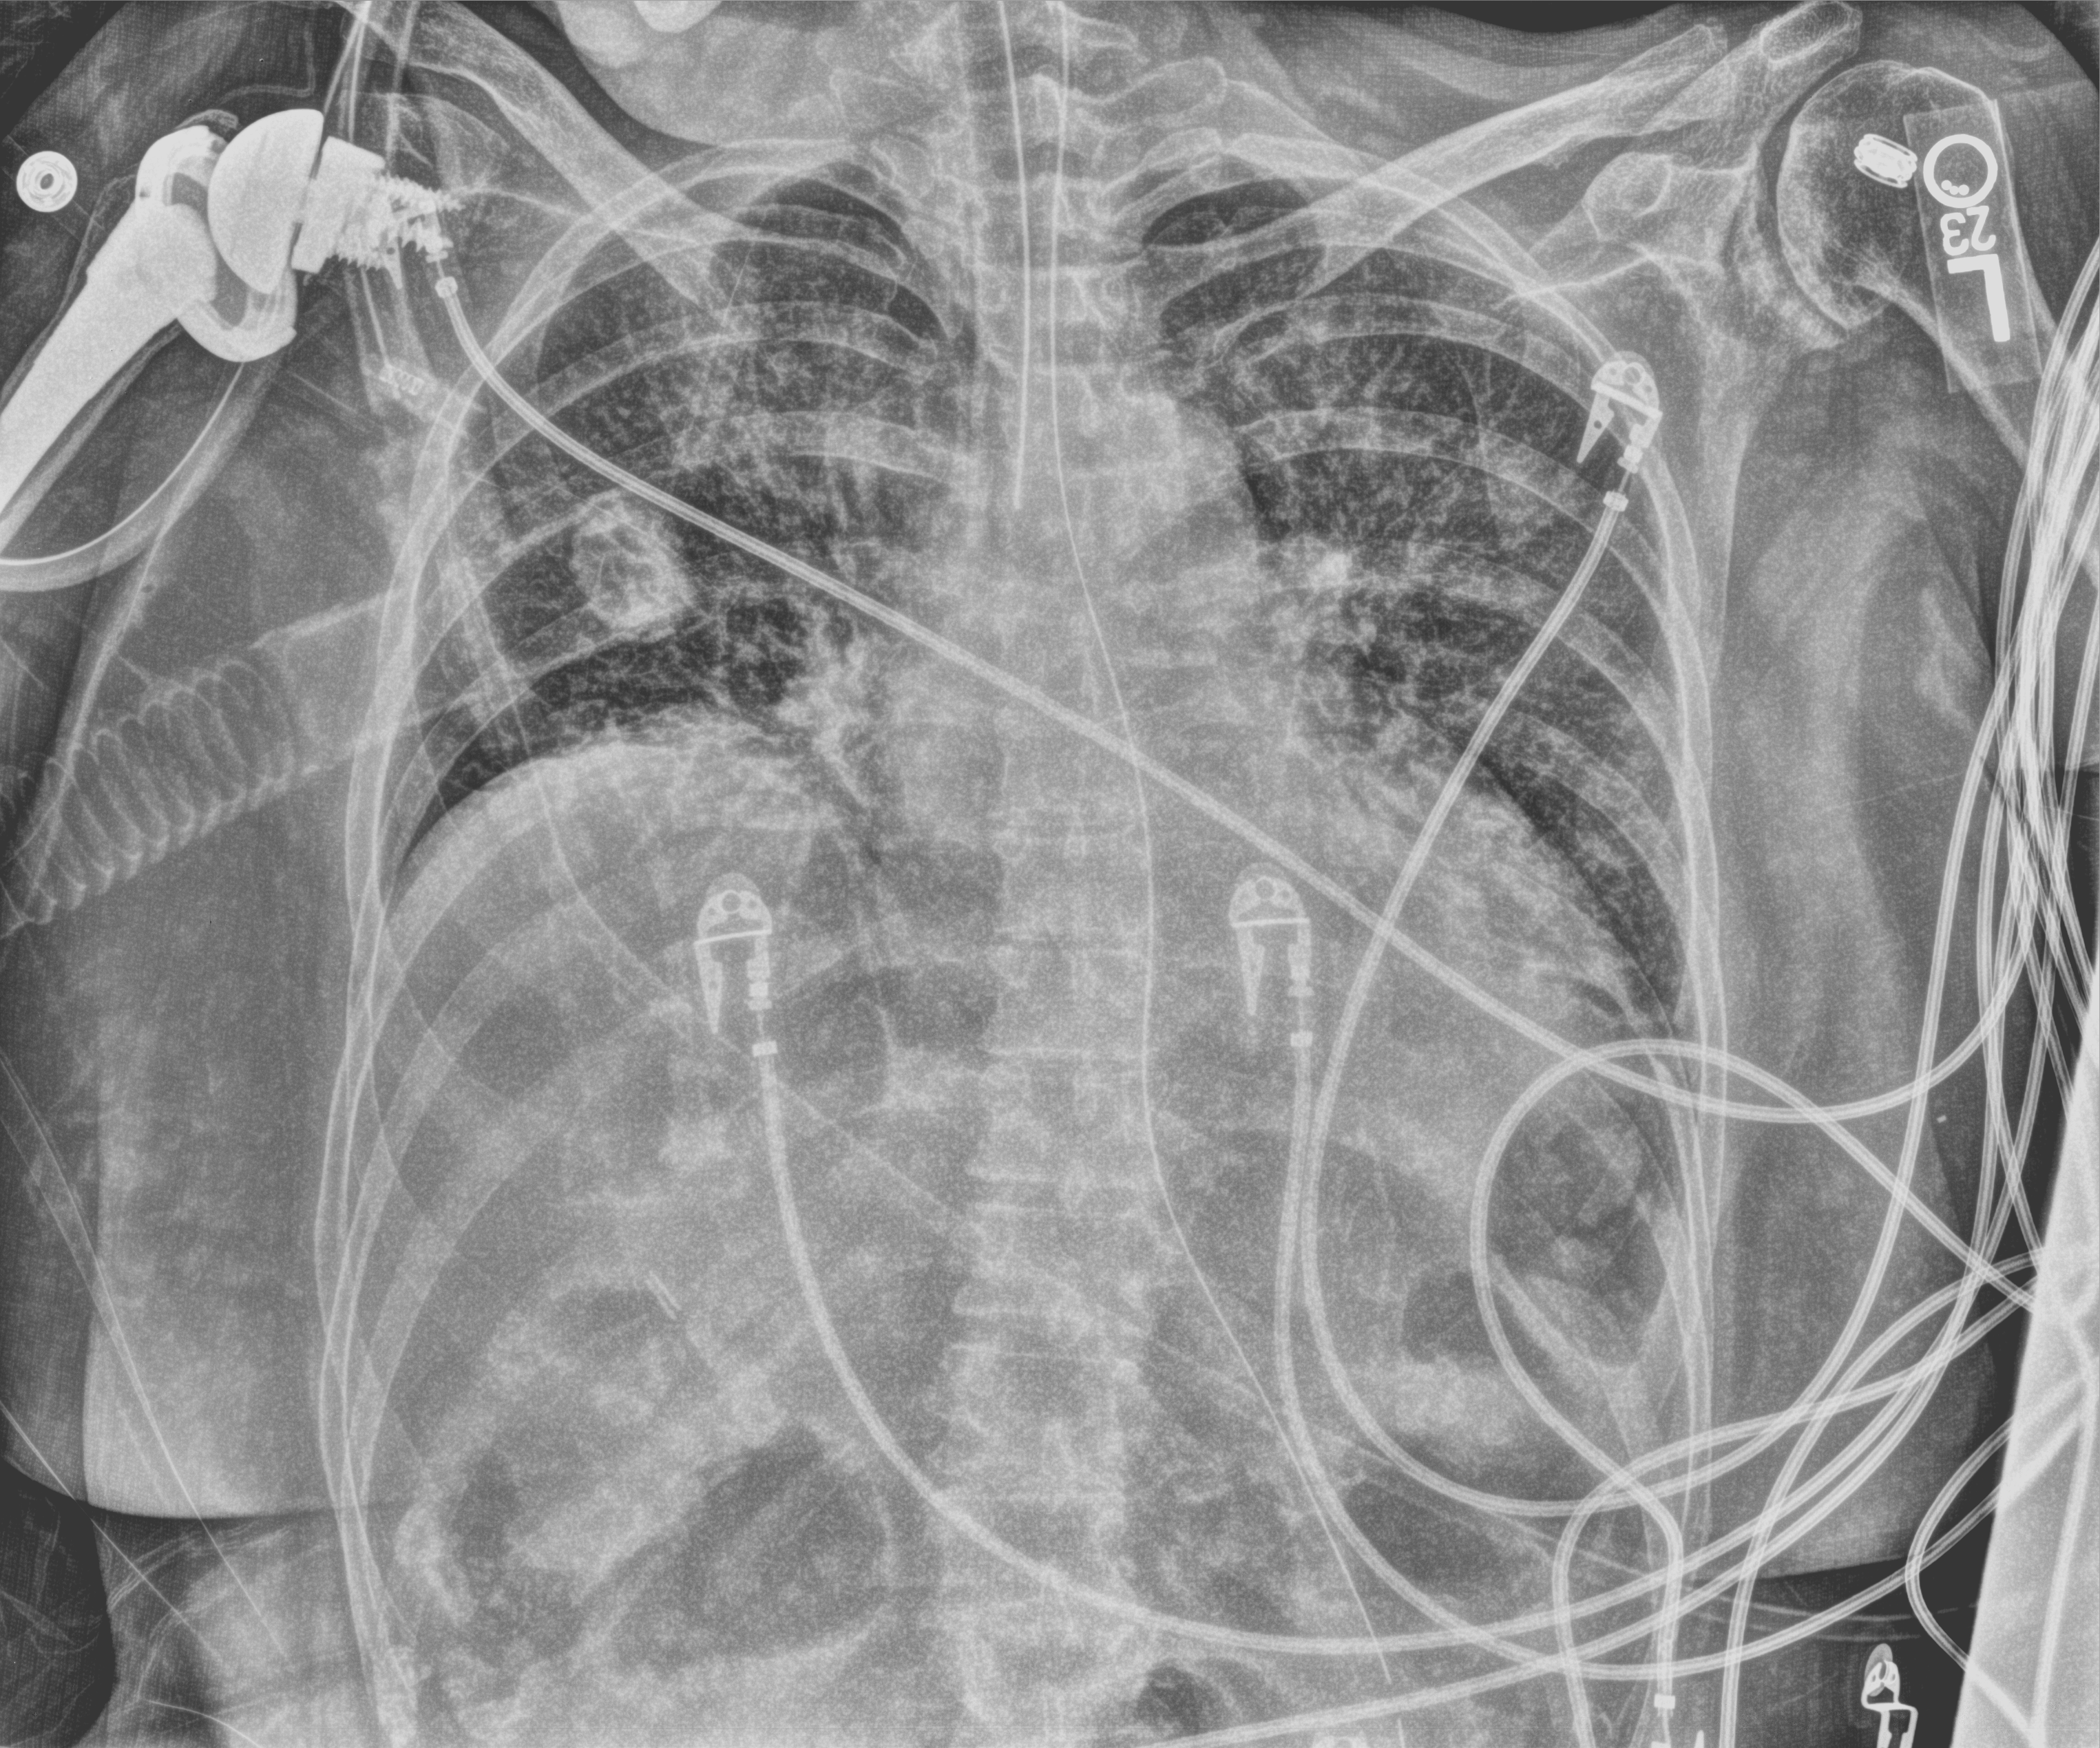
Portable chest radiograph; anteroposterior (AP) projection. Female patient hospitalised with COVID-19, age 60–74 years.
Admission-level facts for this patient (not findings on this image; timing relative to this image not recorded): mechanically ventilated during this hospital stay: yes.